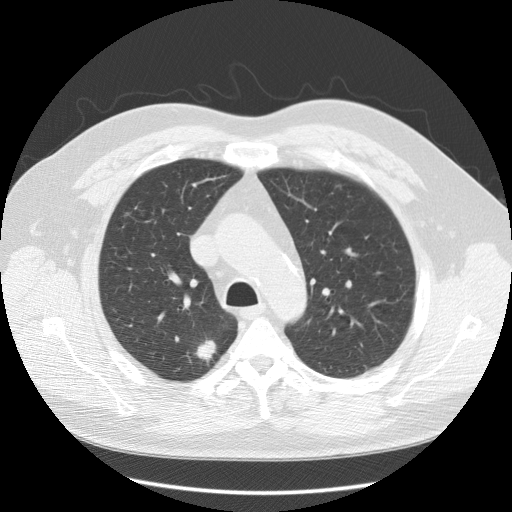
Low-dose screening chest CT, one axial slice; slice 92 of 125 in the series (ordered by position); 120 kVp; lung window (W 1500 / L -600 HU); 2.5 mm slice thickness; 512 × 512 image matrix, field of view 380 × 380 mm.
Annotated regions visible in this slice (outlined manually by an expert reader):
- lesion 1 (tumor, upper lobe of right lung): bounding box [x1, y1, x2, y2] px = [195, 338, 216, 363]